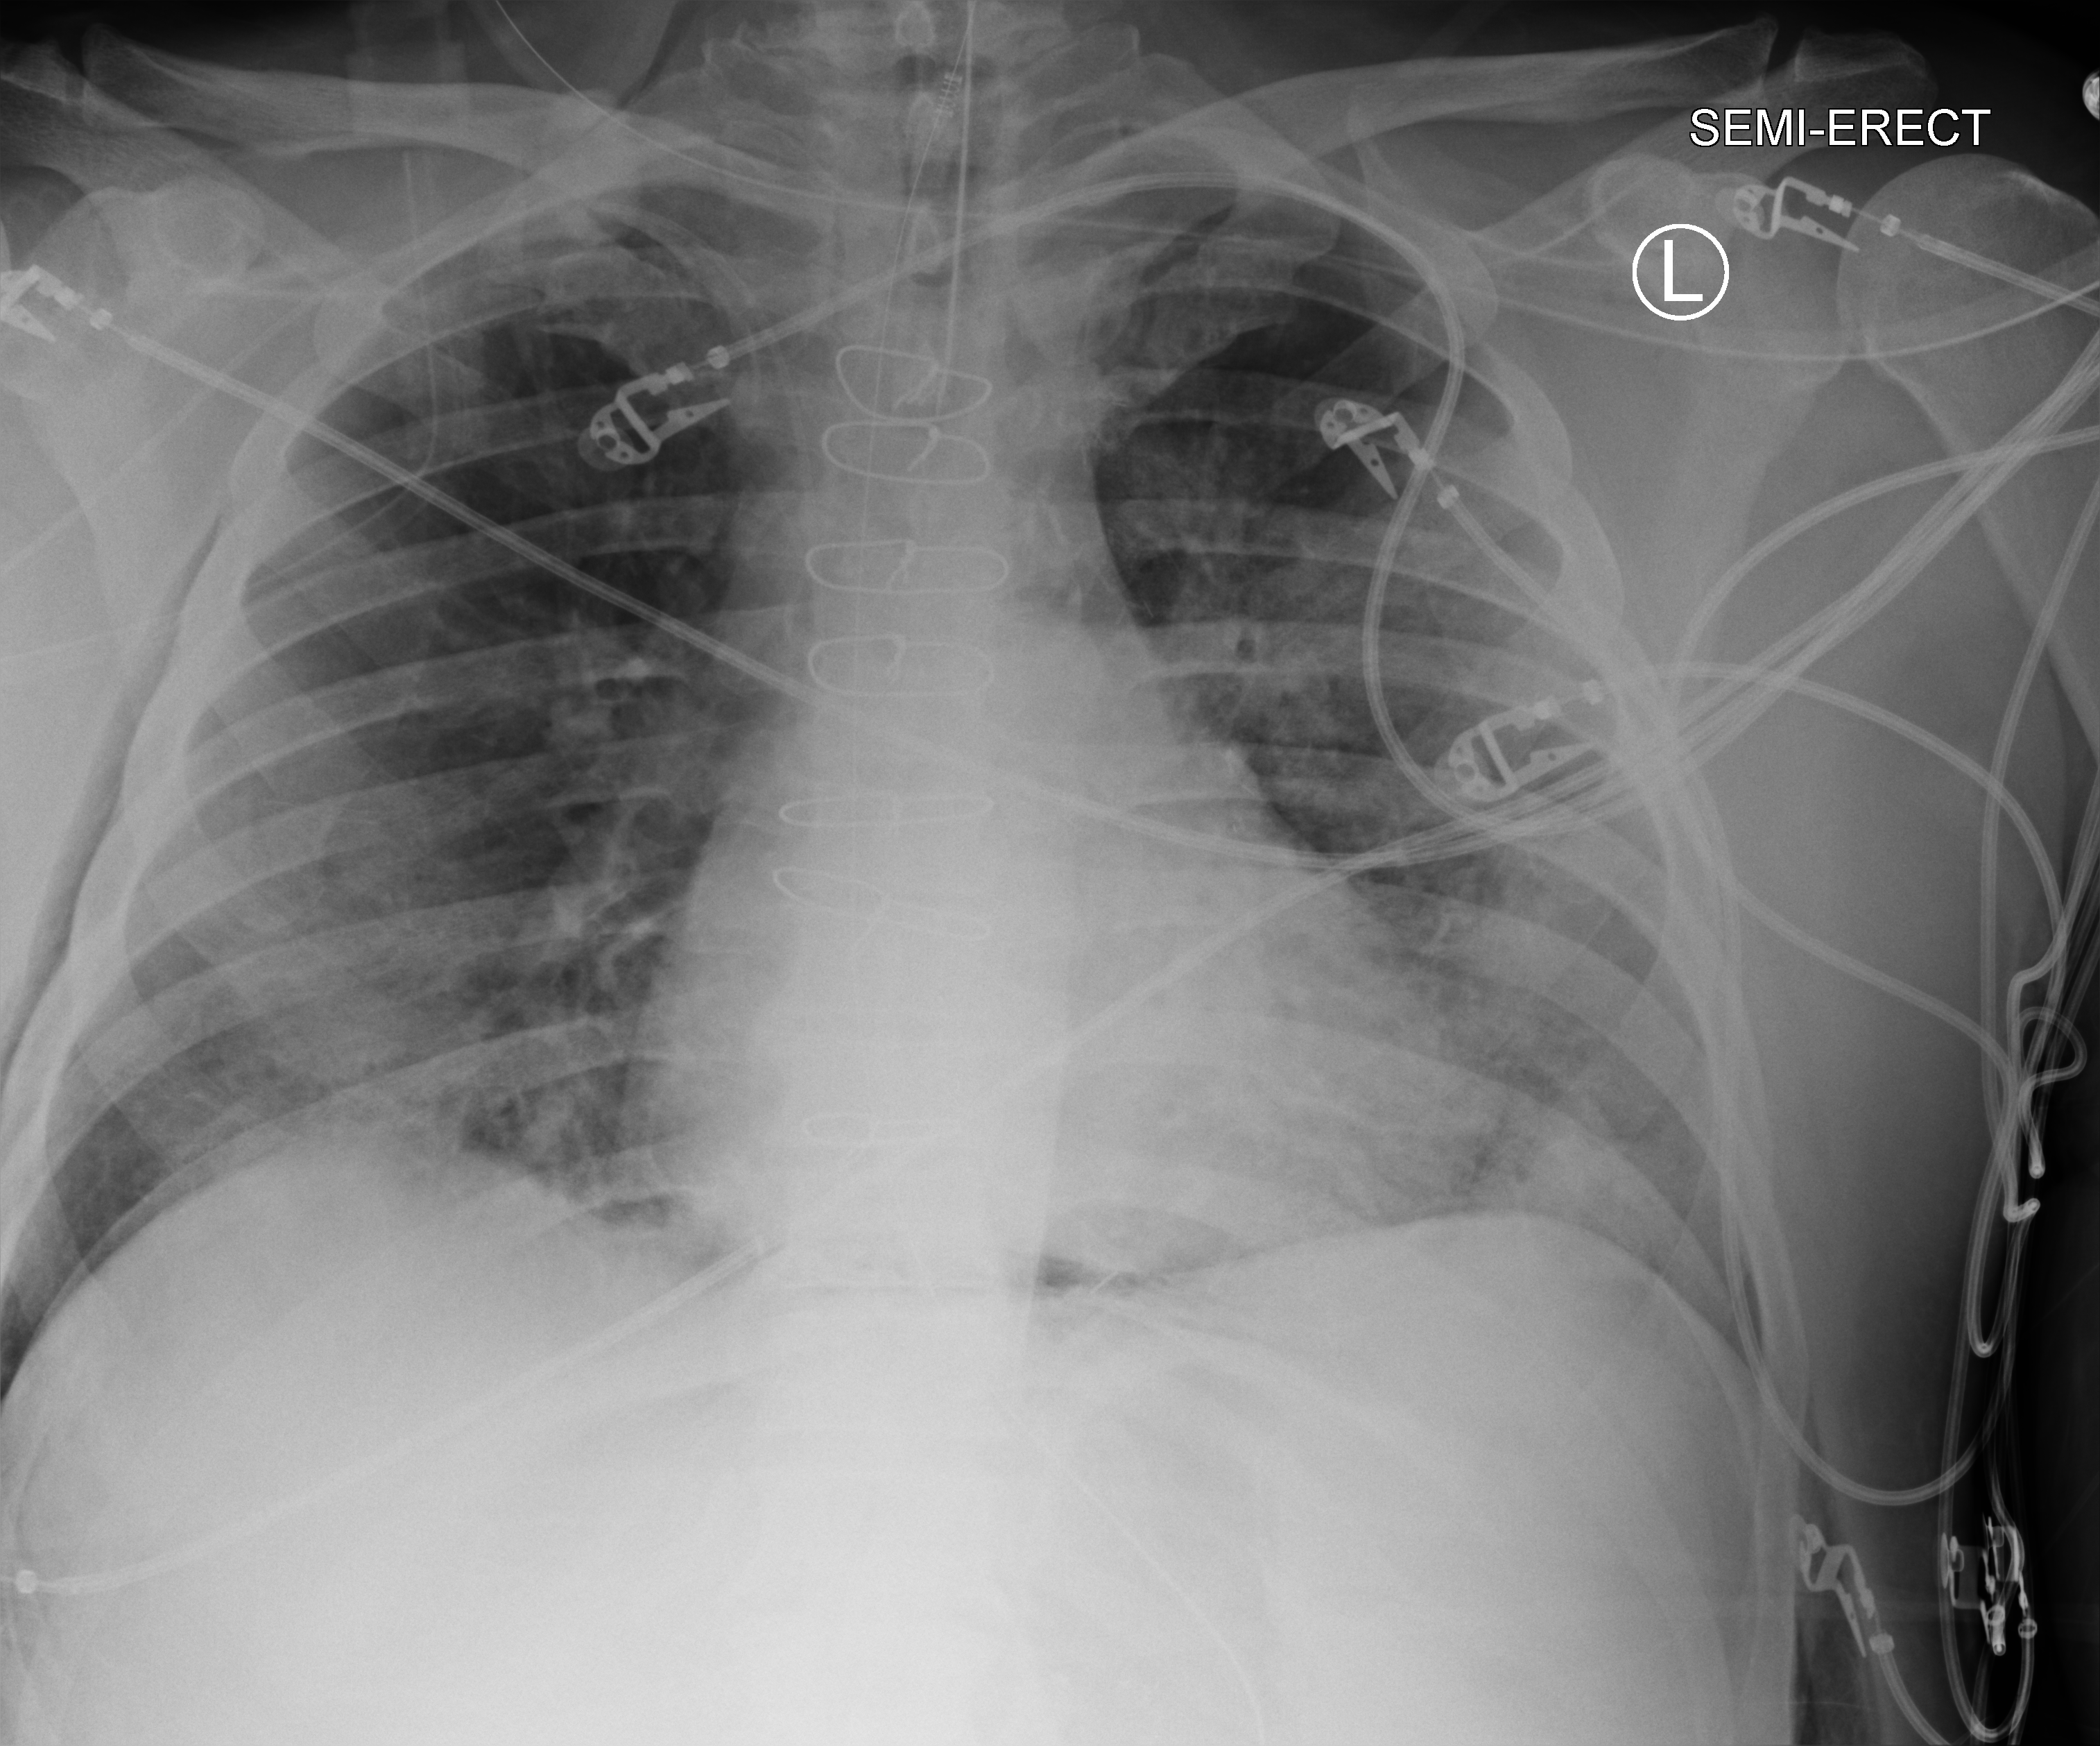
Portable chest radiograph; anteroposterior (AP) projection. Male patient hospitalised with COVID-19, age 60–74 years.
Hospital-stay facts (about this admission, not read from this image; timing relative to this image not recorded): mechanically ventilated during this hospital stay: yes; chronic kidney disease (admission record): no; admitted to intensive care during this hospital stay: yes.